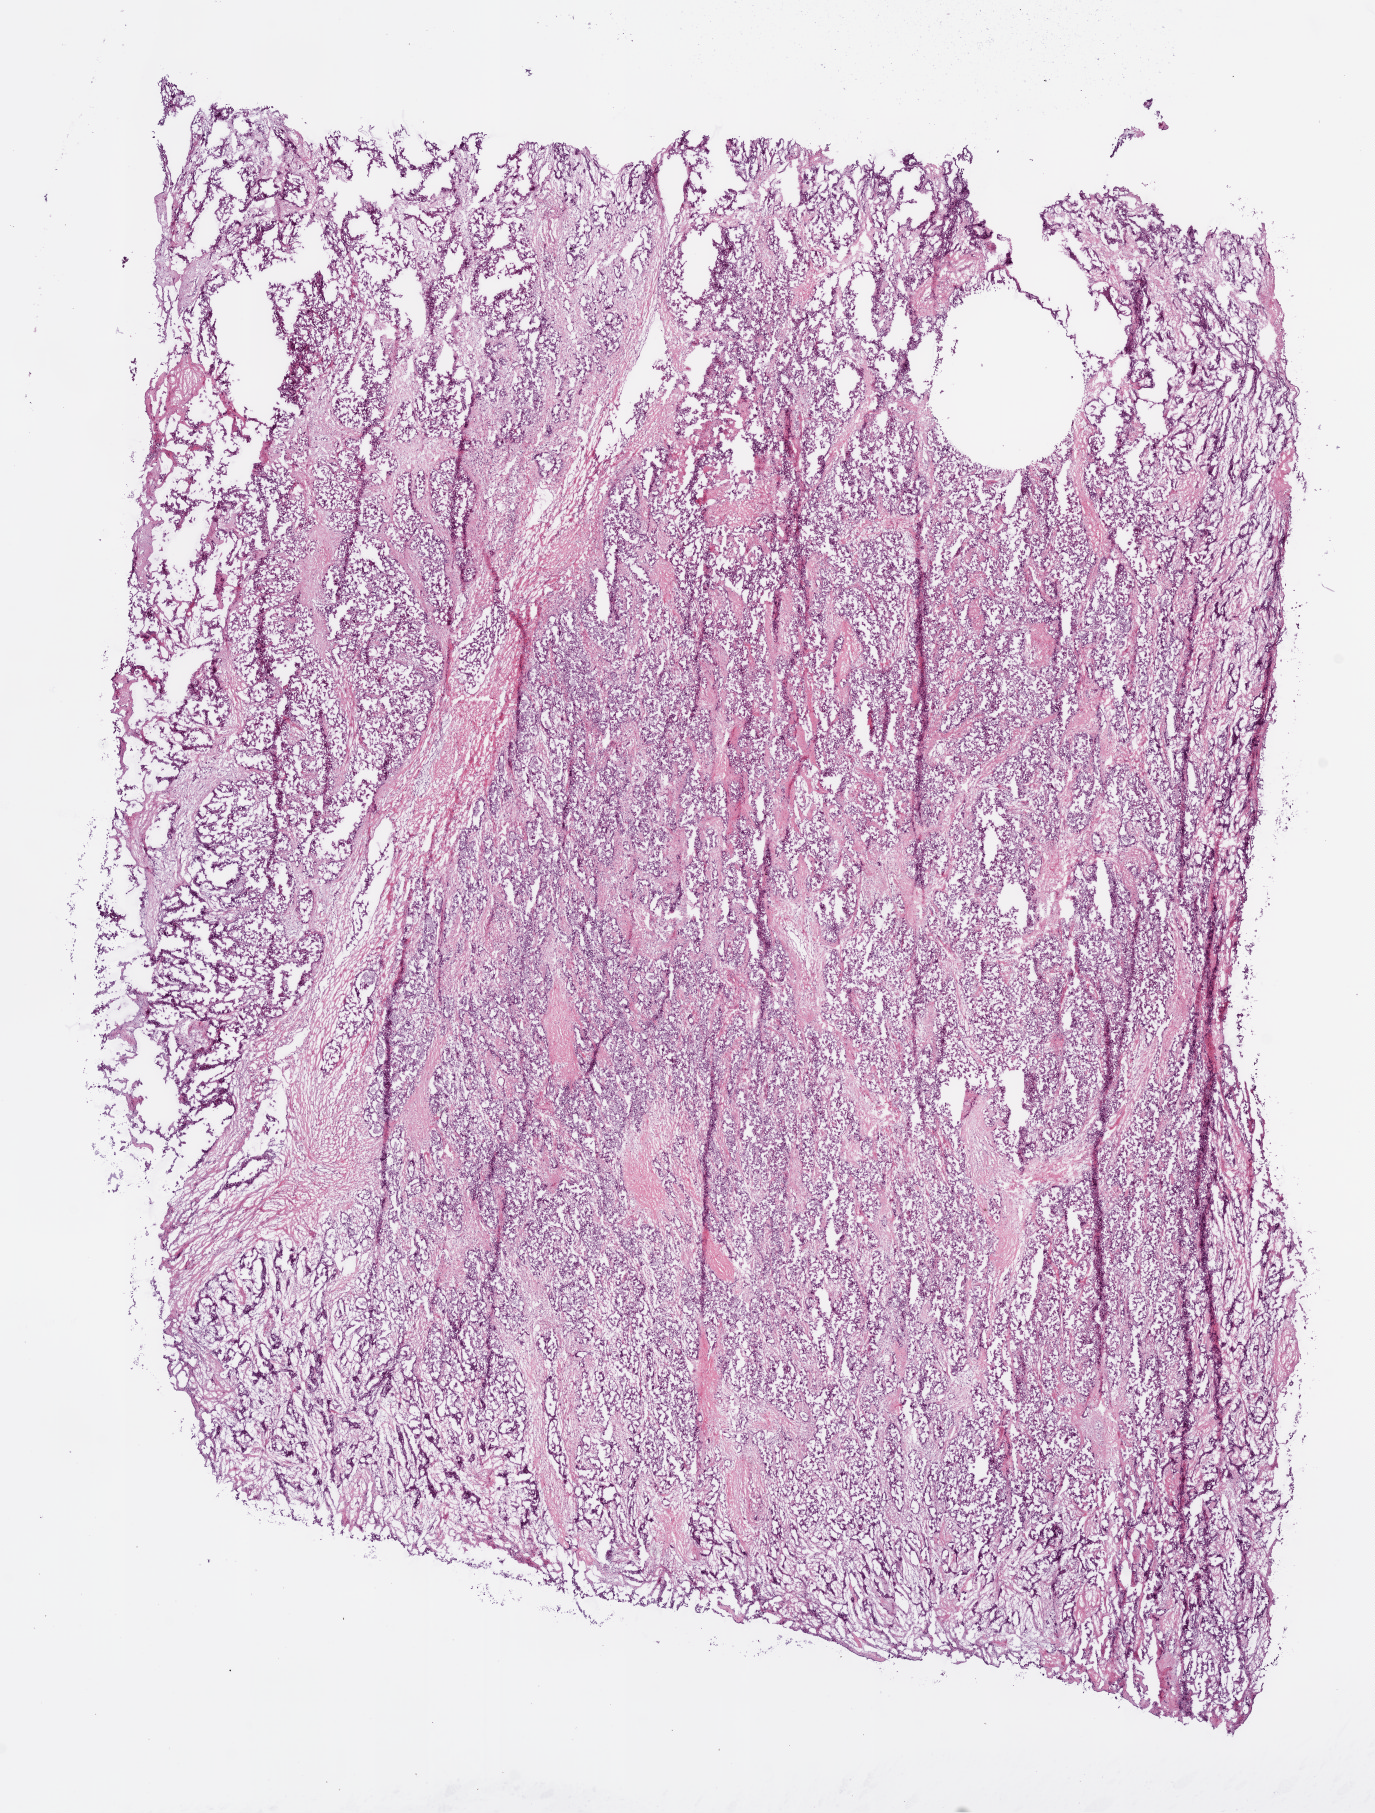
Whole-slide histology image, H&E — a low-resolution overview of the entire scanned area, about 11.0 x 14.5 mm (from a 20x scan); frozen section; primary tumour sample from the liver. Patient: female, age at initial diagnosis 61 years. Histologic grade: G1 (well differentiated). Composition of this section per pathologist review: tumour cells 80%, tumour nuclei 85%, normal cells 0%, stromal cells 15%, necrosis 5%.
Histologic diagnosis: Hepatocellular carcinoma, NOS. AJCC pathologic stage: IIIC.